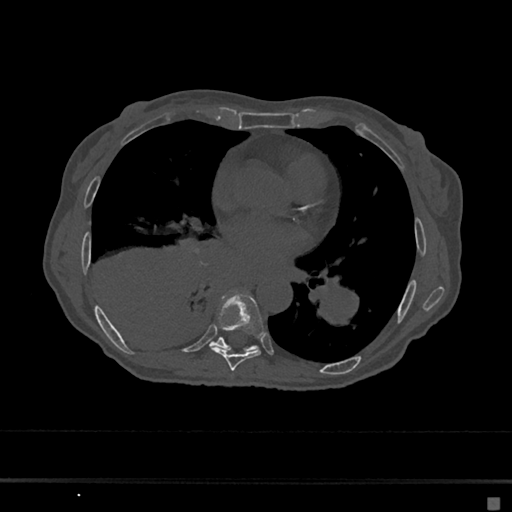
CT including the spine, one axial slice; slice 355 of 797 in the series (ordered by position); reconstruction kernel Br40s/3; 120 kVp; bone window (W 1800 / L 400 HU); 0.5 mm slice thickness; 512 × 512 image matrix, field of view 360 × 360 mm. Female patient, age 68 years. Case-level facts recorded for this patient, not image findings: primary cancer: renal.
Structures marked on this image (semi-automatic segmentation, software-assisted and operator-edited):
- T7 vertebra: bounding box [x1, y1, x2, y2] px = [211, 293, 264, 371]
- T8 vertebra: [211, 338, 257, 351]